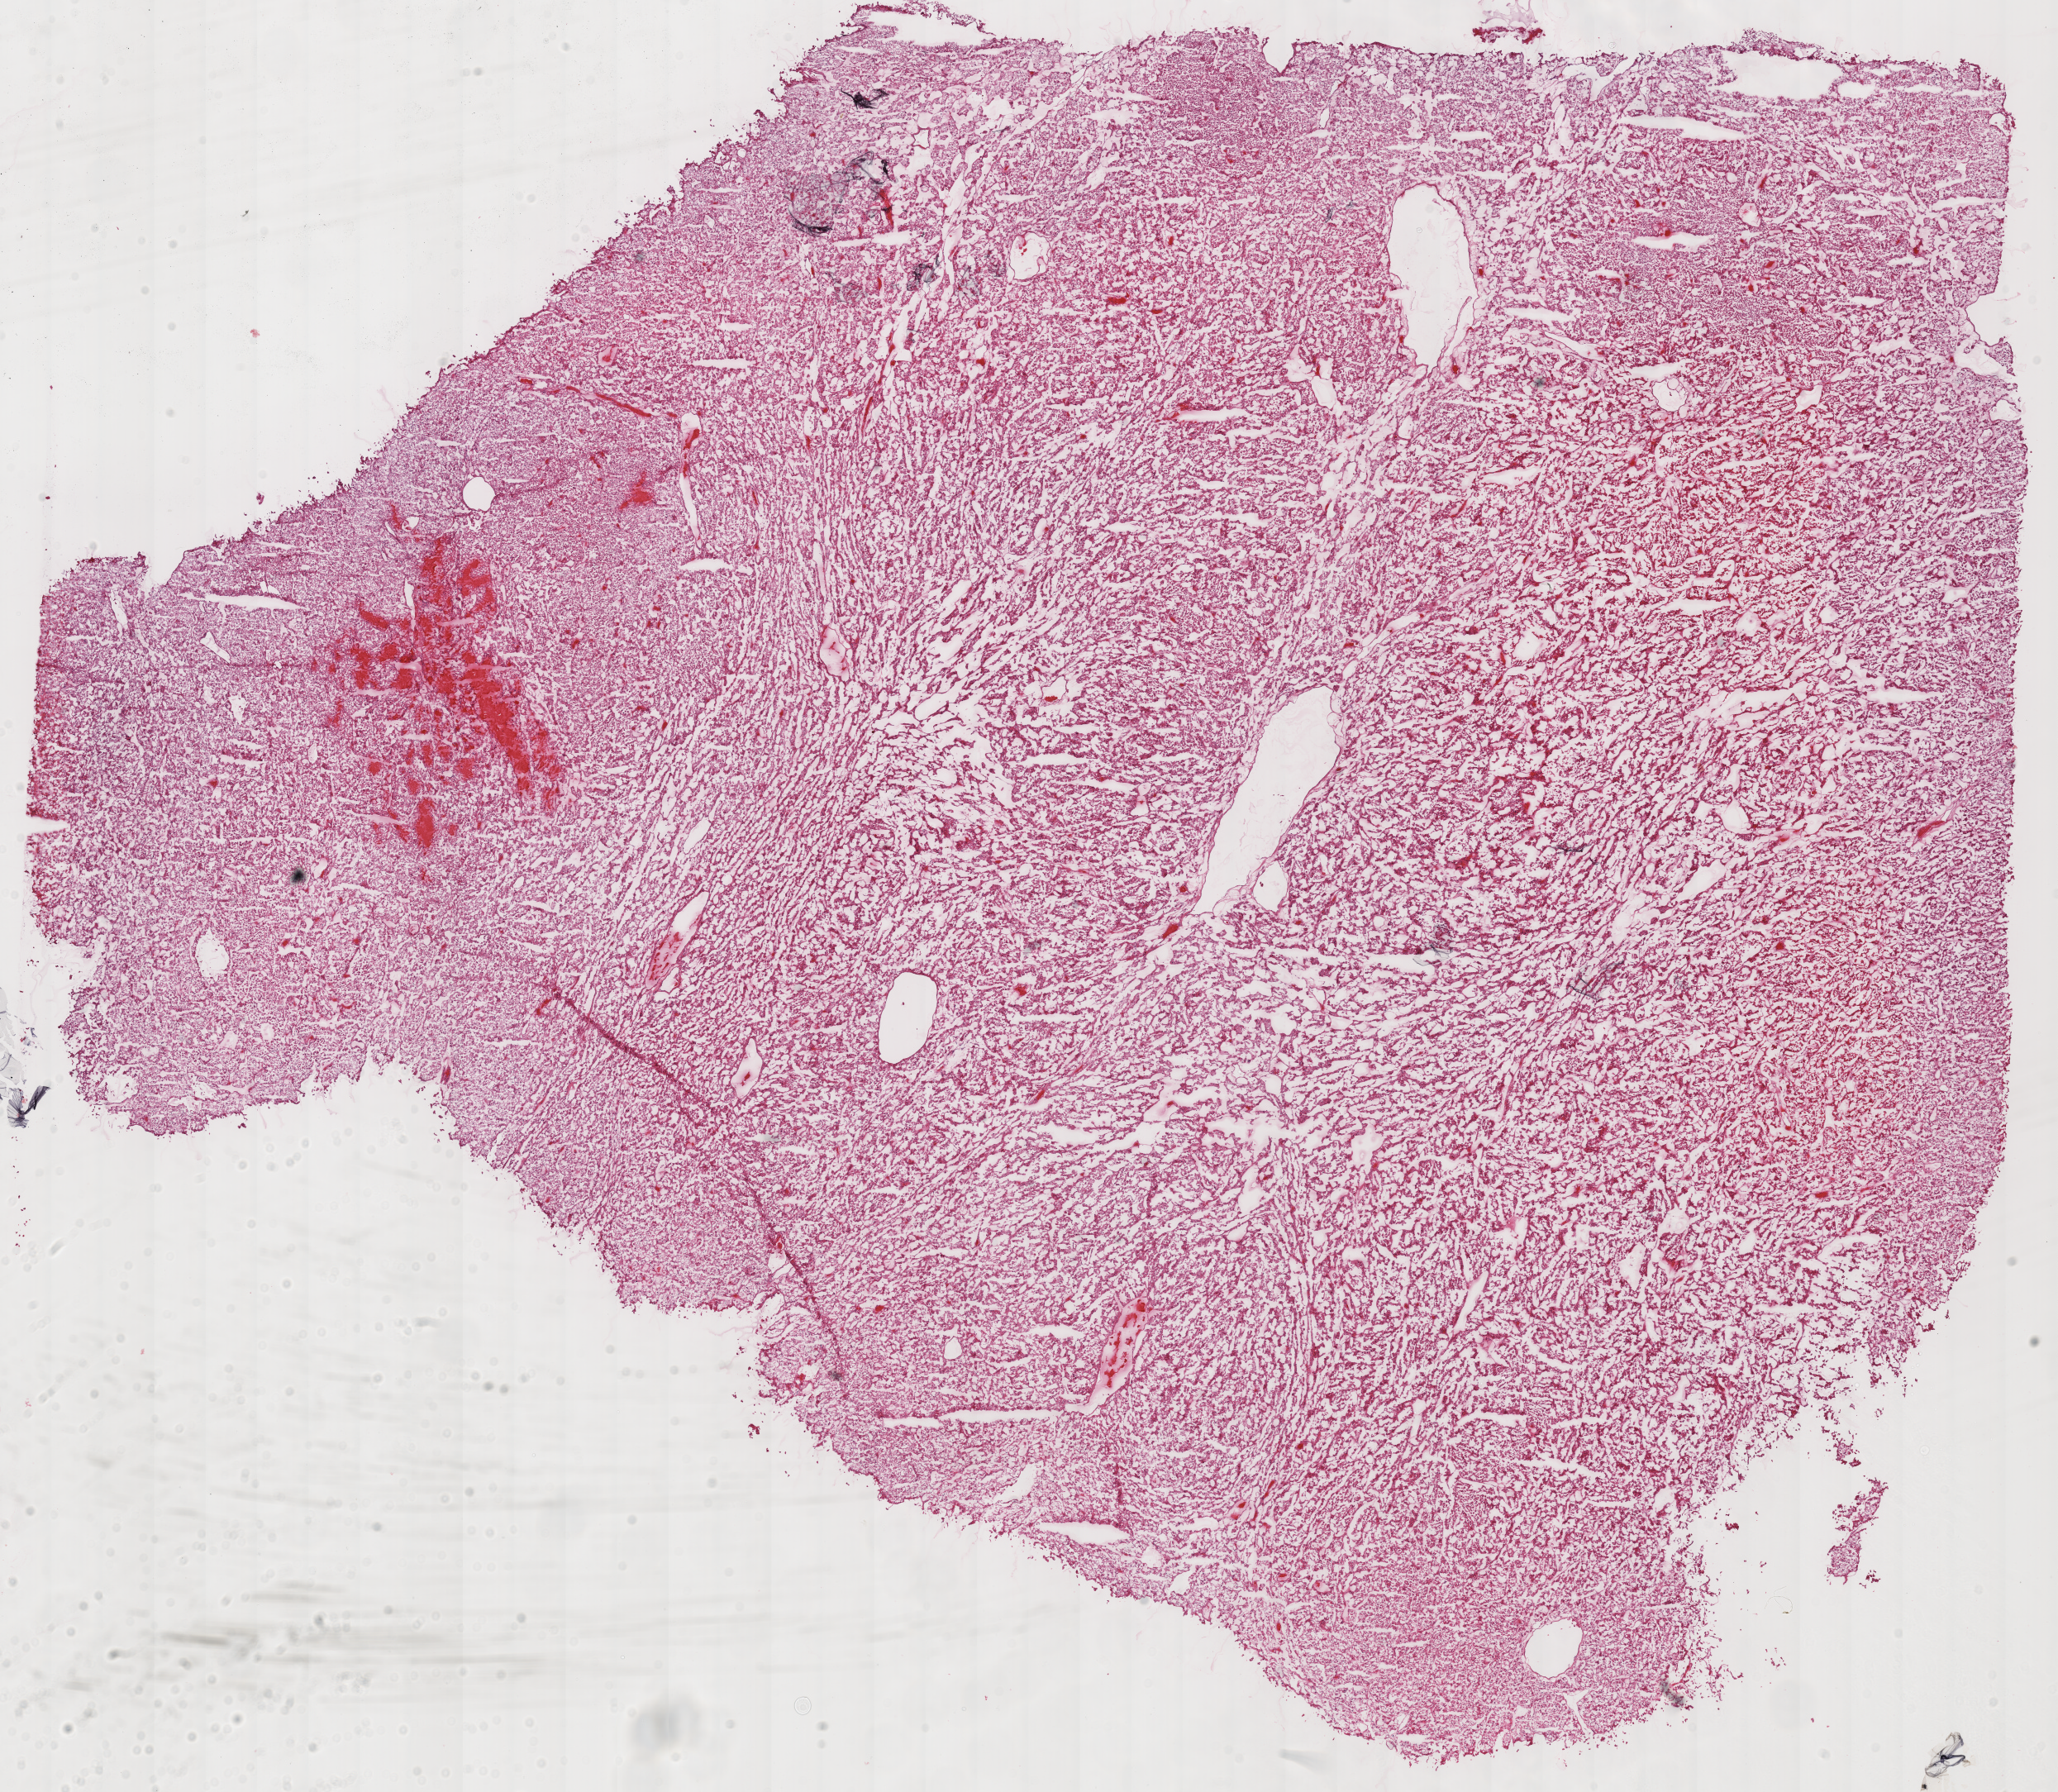
Digitized Hematoxylin and eosin (H&E) stained tissue section (whole slide) — low-resolution overview of the scanned area, about 19.6 x 17.0 mm (from a 40x scan), frozen section, sample: primary tumour, kidney. Female, age 35 years at initial diagnosis. Slide review estimates, as recorded: tumour cells 100%, tumour nuclei 95%, normal cells 0%, stromal cells 0%, necrosis 0%. Inflammatory infiltration, as recorded: lymphocyte infiltration 0%, monocyte infiltration 0%, neutrophil infiltration 0%.
AJCC pathologic stage: II (6th edition). Pathologic diagnosis: Renal cell carcinoma, chromophobe type.